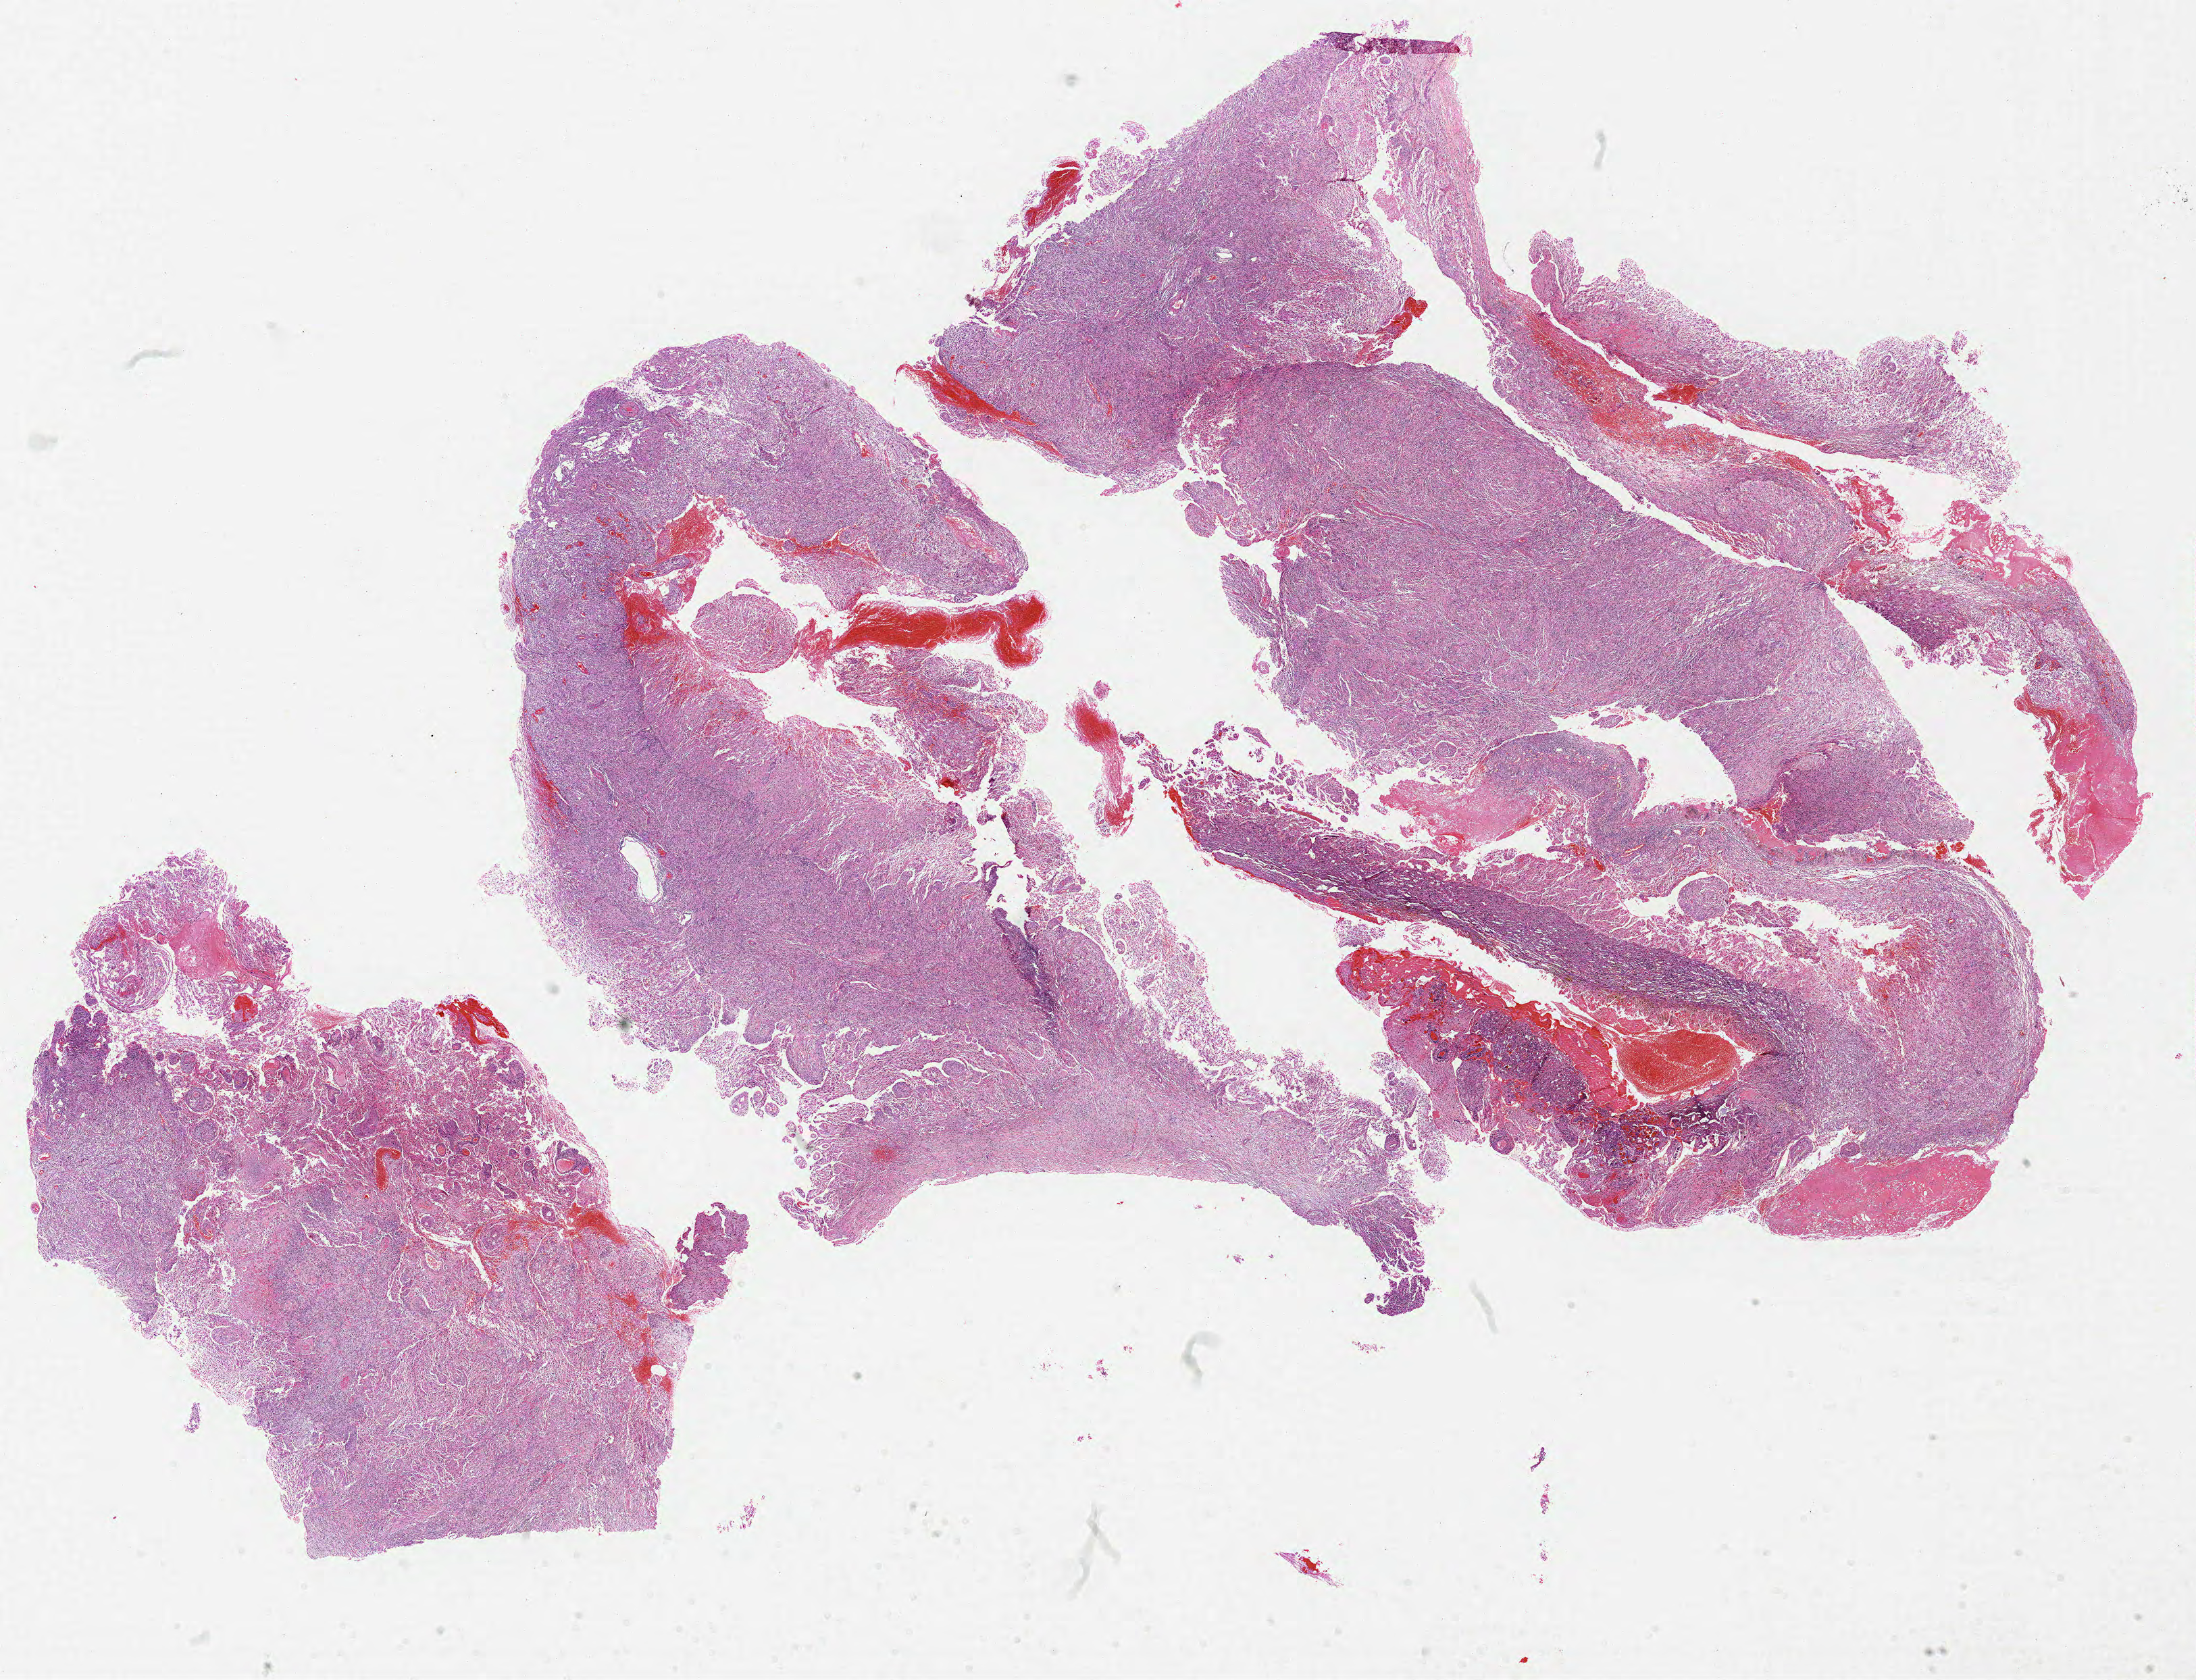
Whole-slide histology image, H&E-stained — low-resolution overview of the scanned area, about 26.0 x 19.9 mm; FFPE section; primary tumour sample from the brain. Female patient; age at initial diagnosis 48 years.
Histologic diagnosis: Glioblastoma.